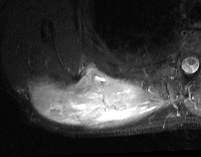
MRI of an extremity soft-tissue mass, one axial slice; position 25 of 74 along the scan axis; STIR; MR volume resampled by the dataset authors to the PET/CT grid (not the native acquisition matrix); 3.27 mm slice thickness; 201 × 157 image matrix. Male patient. Case-level facts recorded for this patient, not image findings: histological type: pleiomorphic spindle cell undifferentiated; grade: high; site of the primary tumour: right parascapusular.
Outlined on this slice (expert contour drawn on MRI and transferred to this co-registered scan by the dataset authors):
- gross tumour volume including surrounding oedema: box from (x=28, y=64) to (x=168, y=129) px
- gross tumour volume (mass): (x=30, y=66)–(x=148, y=126)